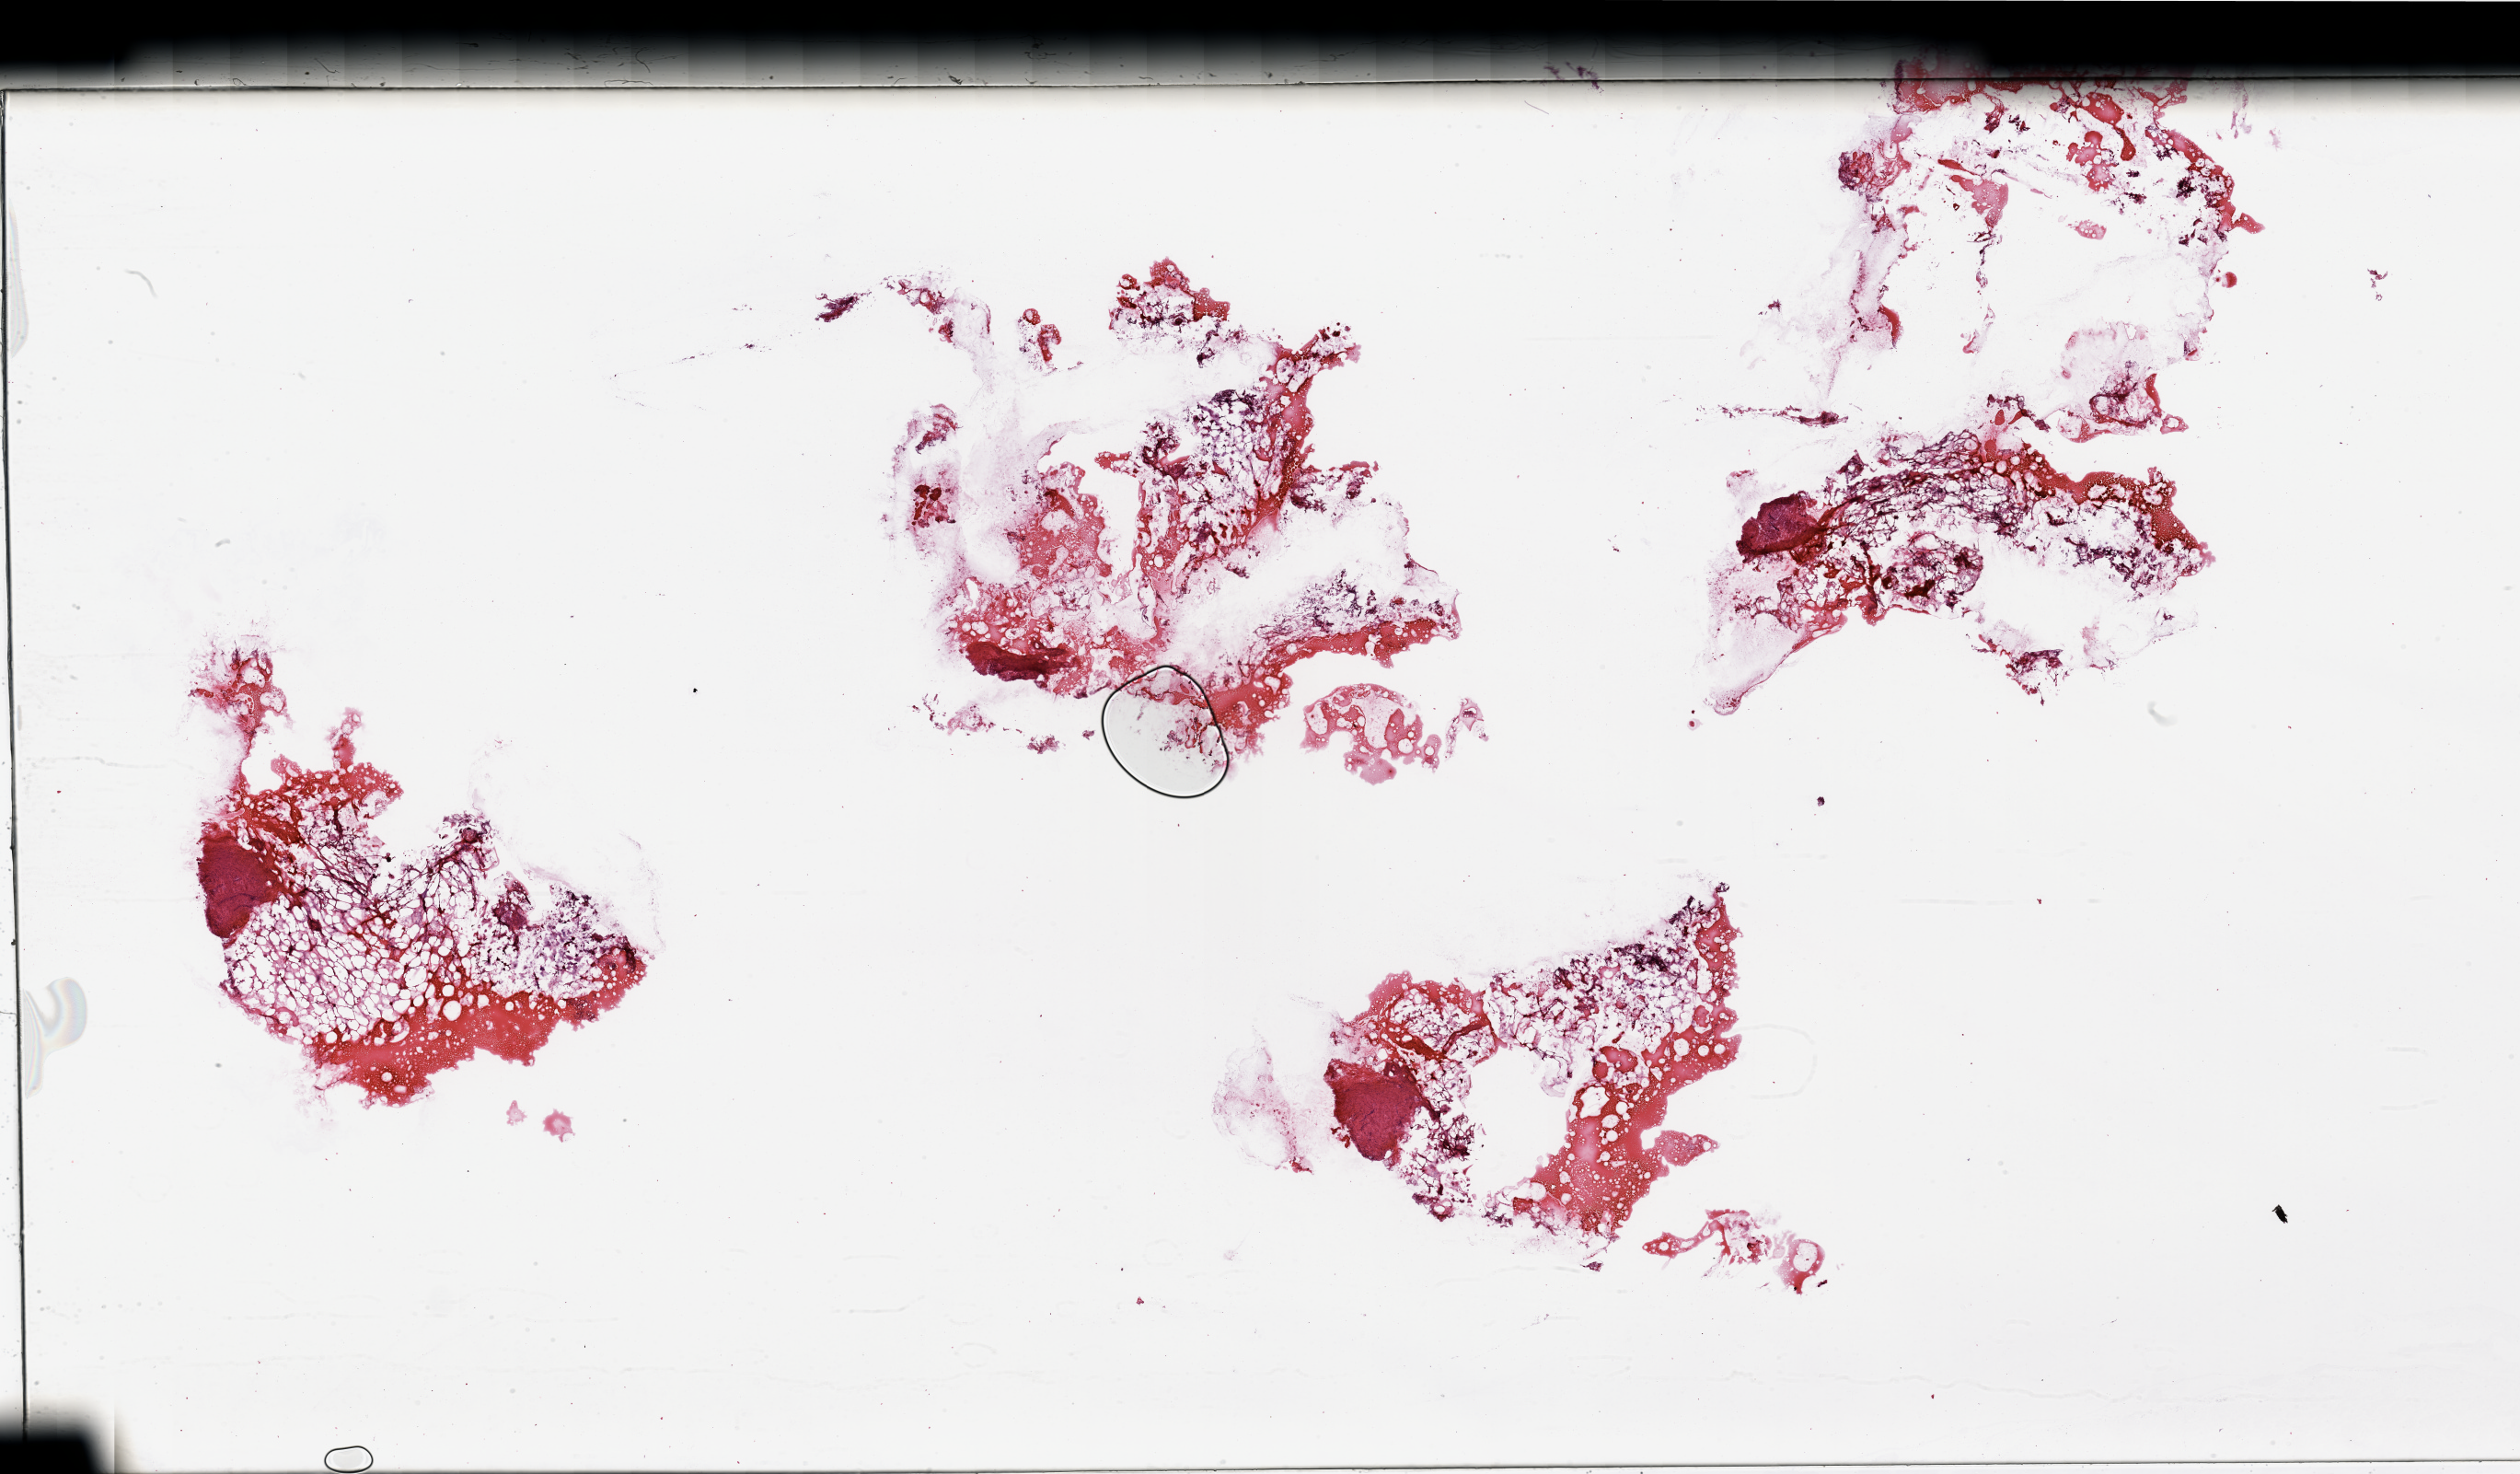
Digitized Hematoxylin and eosin (H&E) stained tissue section (whole slide) — shown as a low-resolution overview of the whole scanned area (about 43.3 x 25.3 mm, slide scanned at 20x), tumour tissue sample, kidney. Female, 74 y/o. Histologic grade: G2 (moderately differentiated).
AJCC pathologic stage: I. Primary tumour site (as recorded): lower pole. Diagnosis: Renal cell carcinoma, NOS.